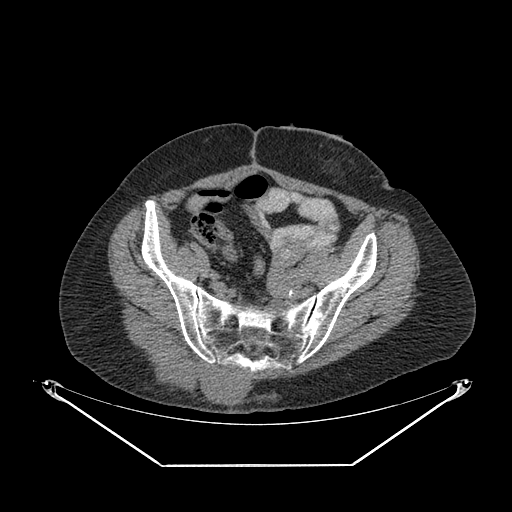
CT of an extremity soft-tissue mass (from a PET/CT study), one axial slice. Position 72 of 267 along the scan axis. Reconstruction kernel SOFT. 140 kVp. Soft-tissue window (W 400 / L 40 HU). 512 × 512 image matrix, field of view 500 × 500 mm. Female patient. Case-level facts recorded for this patient, not image findings: histological type: spindle cell suggestive of myxofibrosarcoma; grade: intermediate; site of the primary tumour: right buttock.
Structures marked on this image (expert contour drawn on MRI and transferred to this co-registered scan by the dataset authors):
- gross tumour volume (mass): bounding box <137,347,250,407> (left, top, right, bottom; pixels)